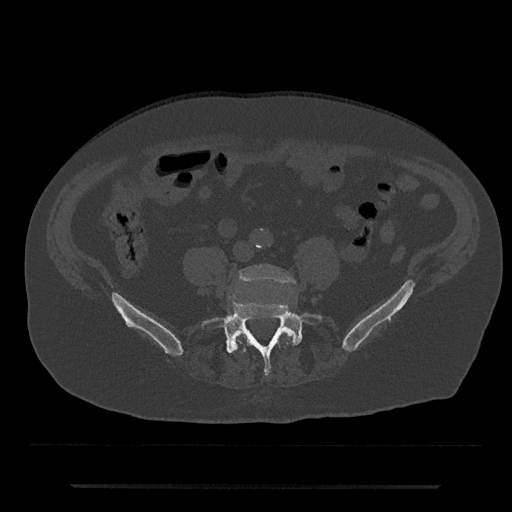
CT including the spine, one axial slice; slice 306 of 797 in the series (ordered by position); reconstruction kernel Br40s/3; 120 kVp; bone window (W 1800 / L 400 HU); 0.5 mm slice thickness; 512 × 512 image matrix. Male patient, age 80 years. From the clinical record (not read from this slice): primary cancer: prostate; vertebrae with lytic lesions (as recorded): L1, T11.
Annotated regions visible in this slice (semi-automatically segmented with operator editing):
- L4 vertebra: bounding box [x1, y1, x2, y2] px = [237, 265, 296, 344]
- L5 vertebra: [201, 301, 323, 375]